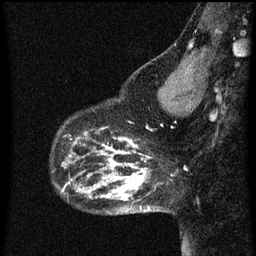
Breast MRI (dynamic contrast-enhanced), one sagittal slice. Slice 16 of 60 in the series (ordered by position). Dynamic contrast-enhanced series, image 2 of 3 at this slice position (ordered by acquisition). 1.5 T. TE 4.2 ms, TR 8 ms. 2 mm slice thickness. 256 × 256 image matrix. Patient: female, 43 years.
Annotated regions visible in this slice (semi-automatically segmented with operator editing):
- analysis volume of interest (the breast-tissue region the enhancement analysis was run in; not a lesion): bounding box <53,108,101,155> (left, top, right, bottom; pixels)
- tumour enhancement mask (voxels above the 70 % enhancement threshold inside the analysis volume of interest): <77,136,101,153>